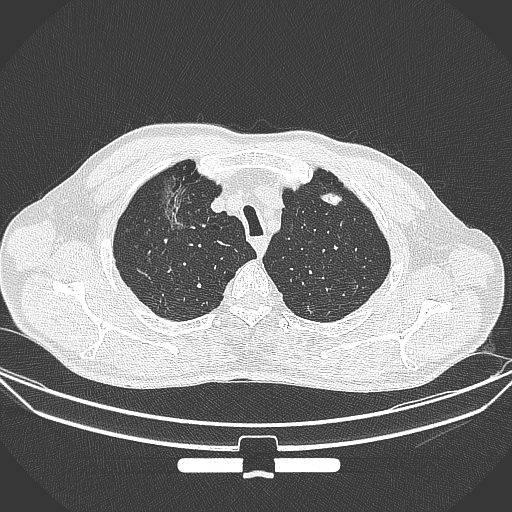
Chest CT, one axial slice; slice 291 of 355 in the series (ordered by position); 120 kVp; lung window (W 1500 / L -600 HU); 1 mm slice thickness; 512 × 512 image matrix, field of view 399 × 399 mm. Patient: male, 67 years. Case-level facts recorded for this patient, not image findings: clinical TNM (as recorded): T1c N0 M0; histopathological grade: G2.
Structures marked on this image (bounding box drawn by a radiologist):
- lung tumour (recorded histology: adenocarcinoma): box from (x=155, y=177) to (x=195, y=236) px